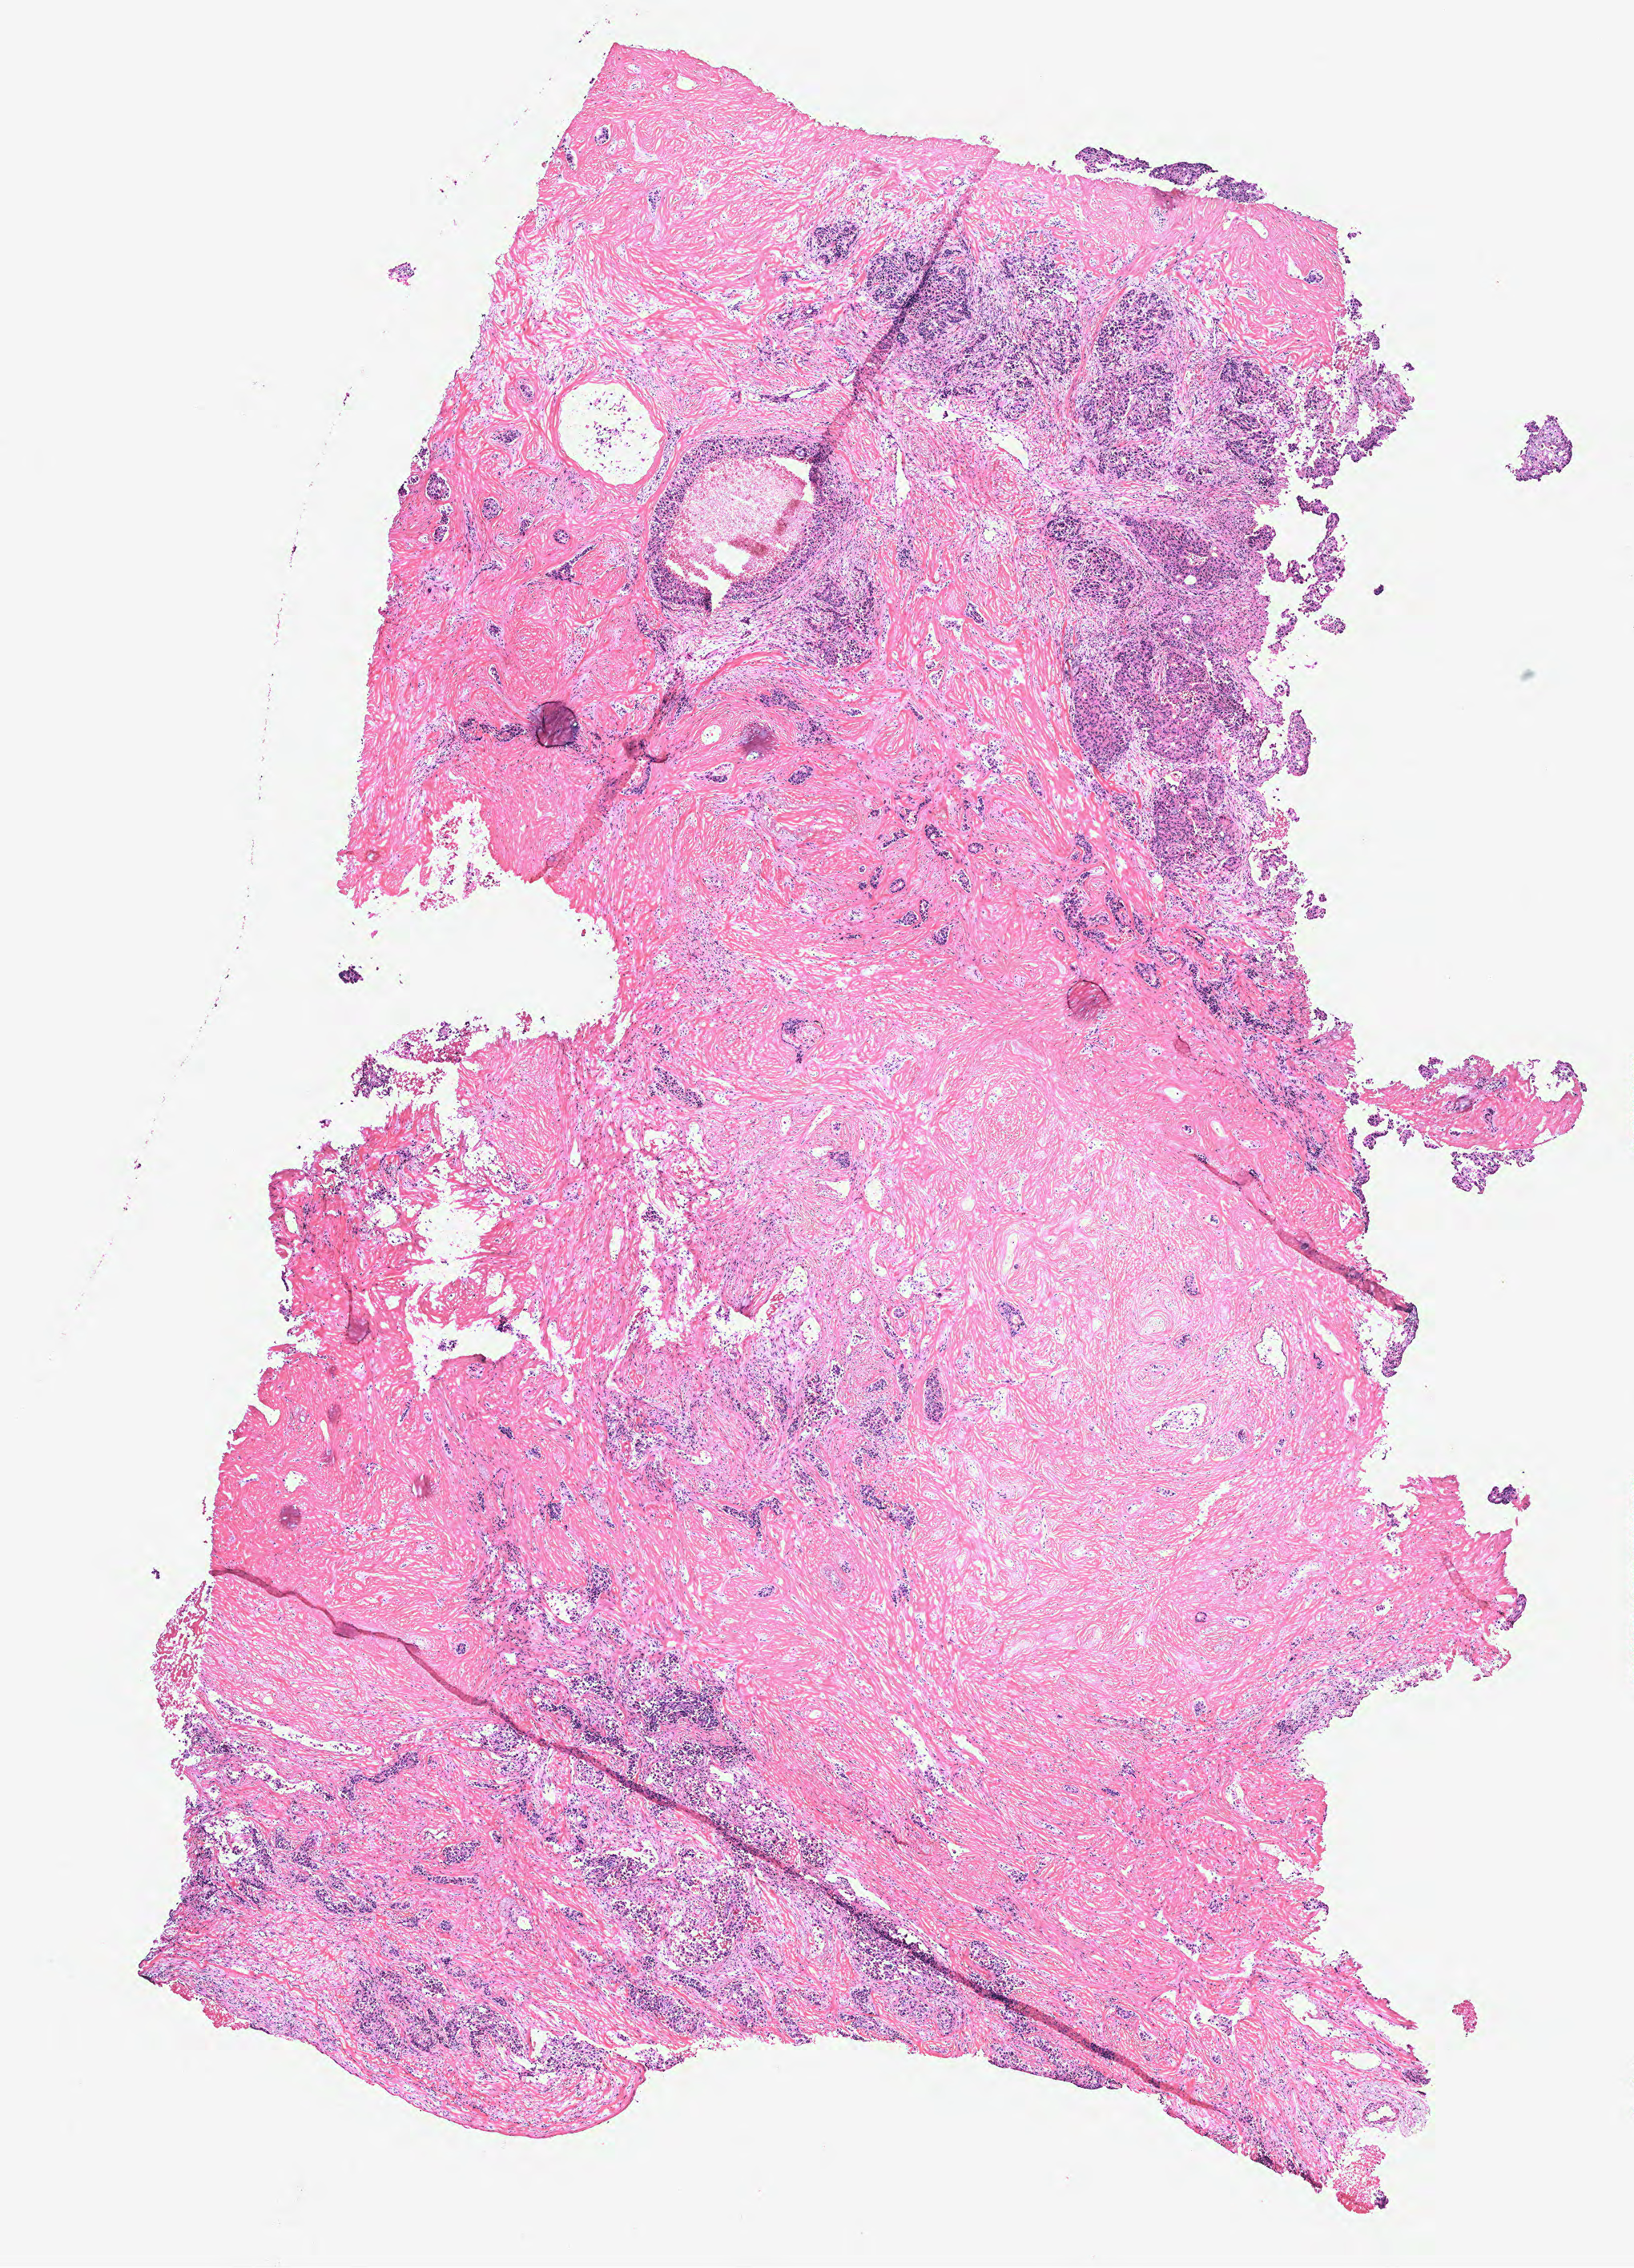
Whole-slide histology image, Hematoxylin and eosin (H&E) stained, a low-resolution overview of the entire scanned area, about 8.2 x 11.3 mm, tumour tissue sample, breast. Female, 71 y/o.
* AJCC pathologic stage: IIIB
* histologic diagnosis: Intraductal papillary carcinoma